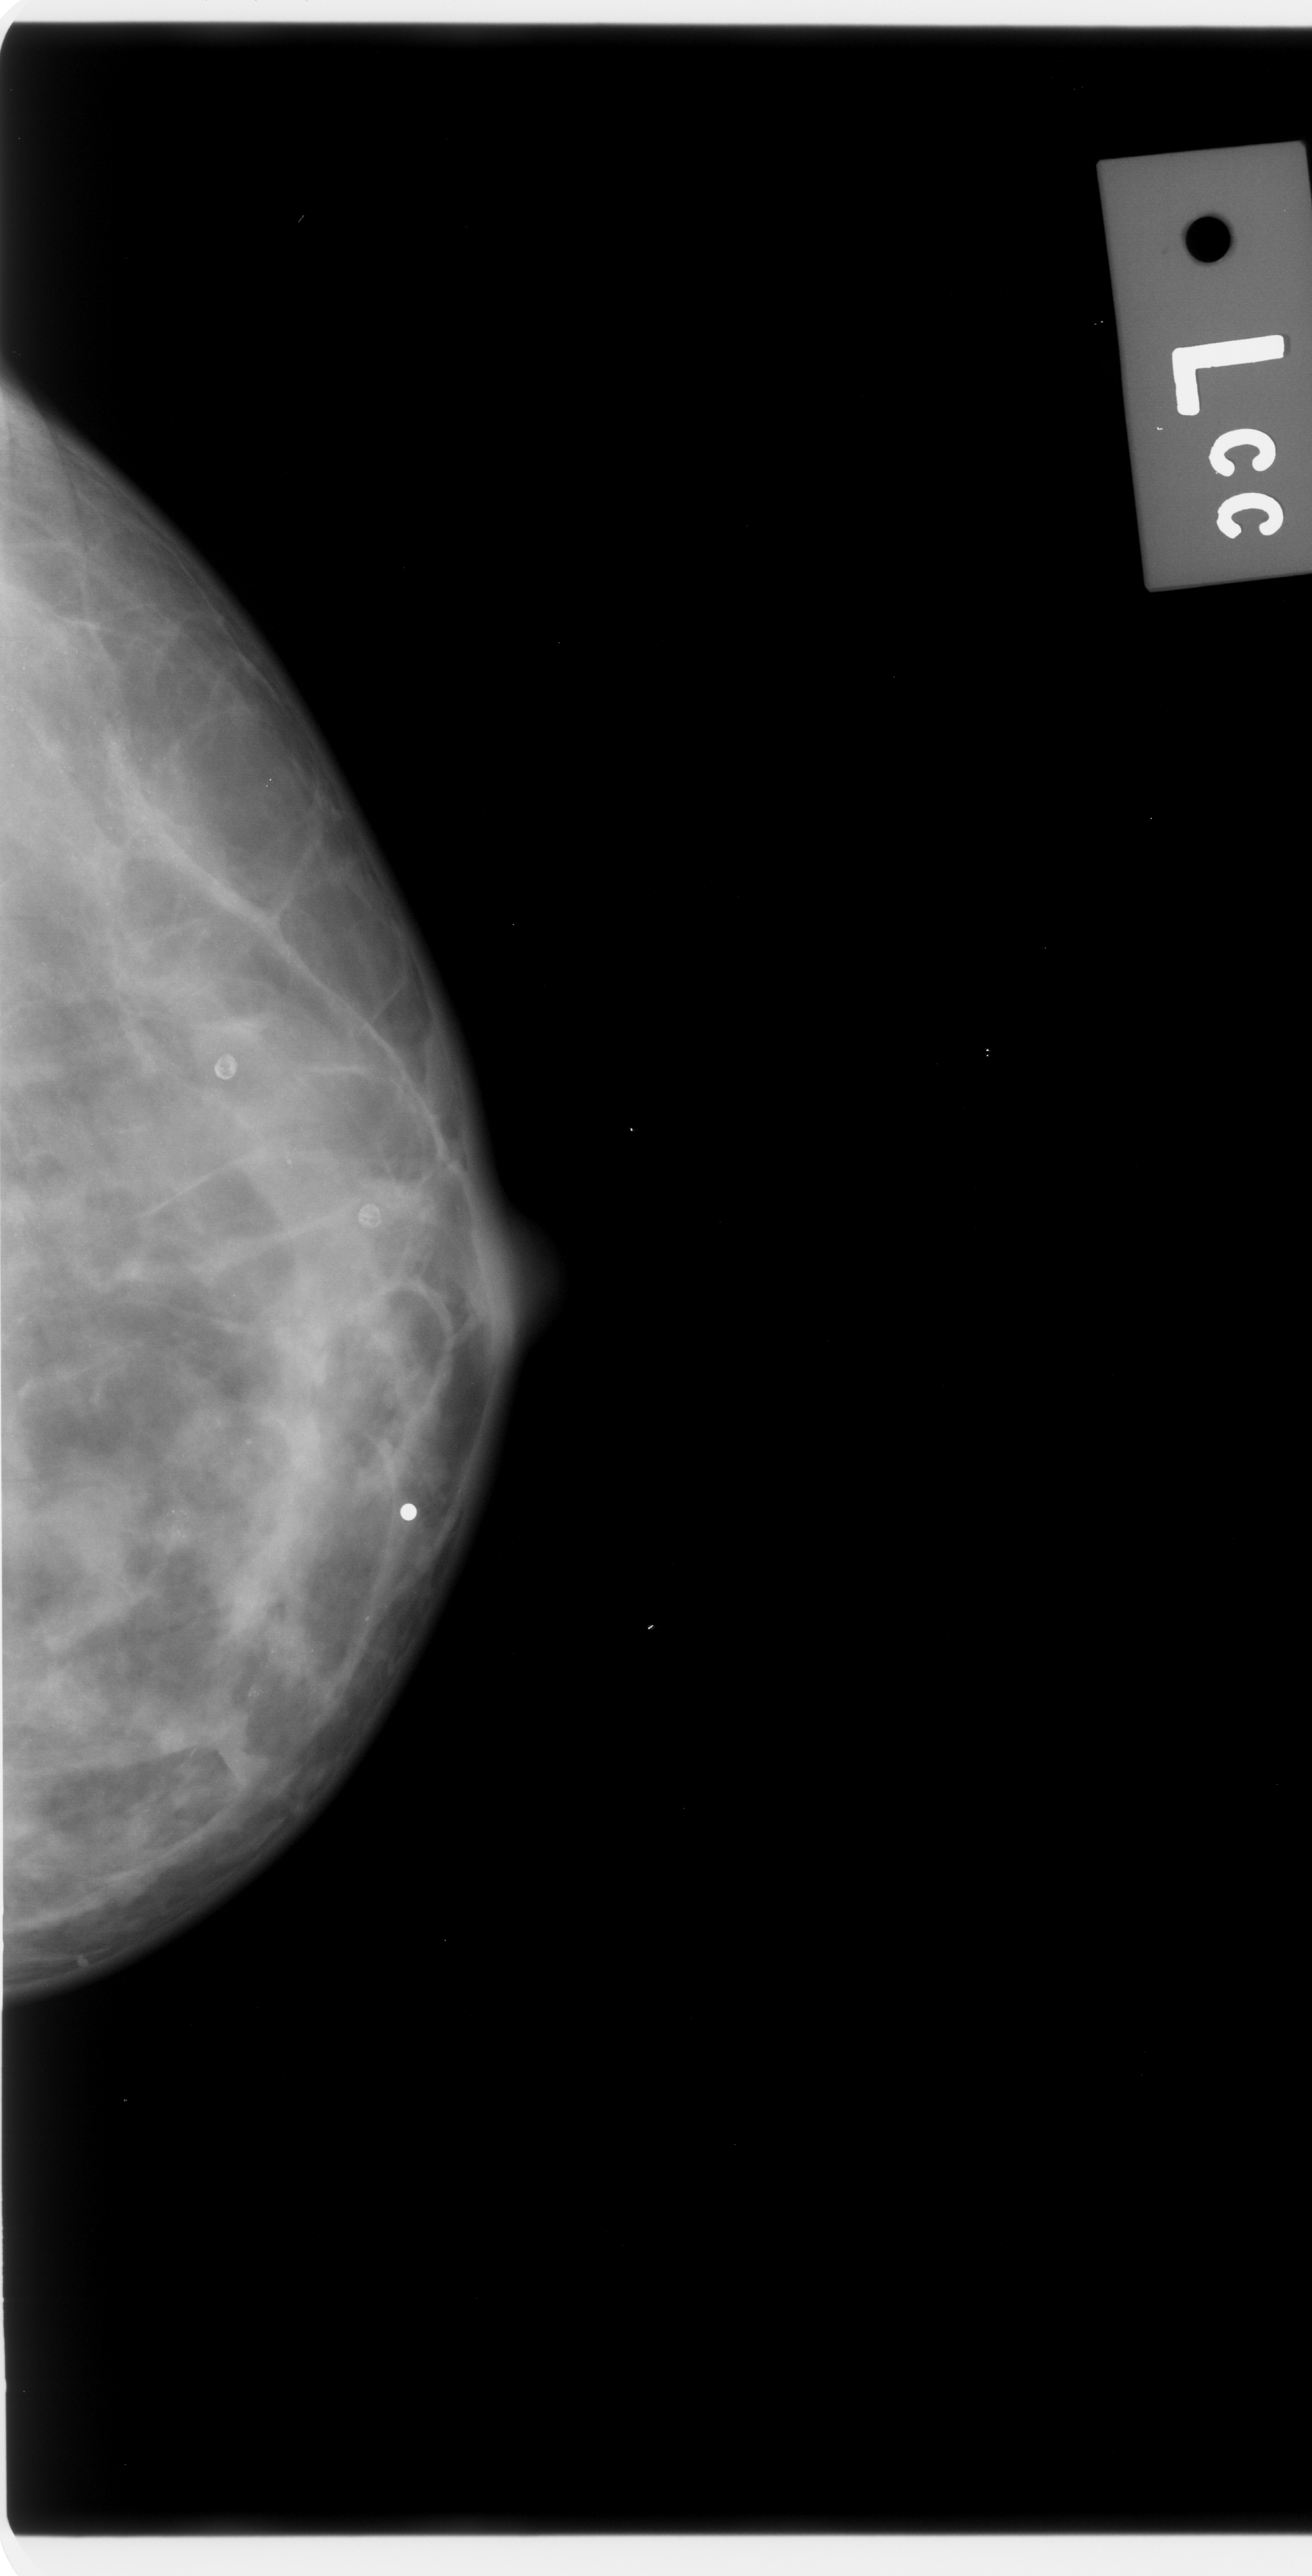
Mammogram (digitized film); left breast; craniocaudal (CC) view; BI-RADS breast density category 2 (scale 1–4); 1312 × 2576 image matrix.
Expert-marked regions of interest on this film, with their recorded descriptors:
- calcifications, morphology amorphous, distribution diffusely scattered; BI-RADS assessment category 3; pathology result (as recorded, not read from the image): malignant: bounding box (x1, y1, x2, y2) in pixels: (0, 462, 454, 1814)